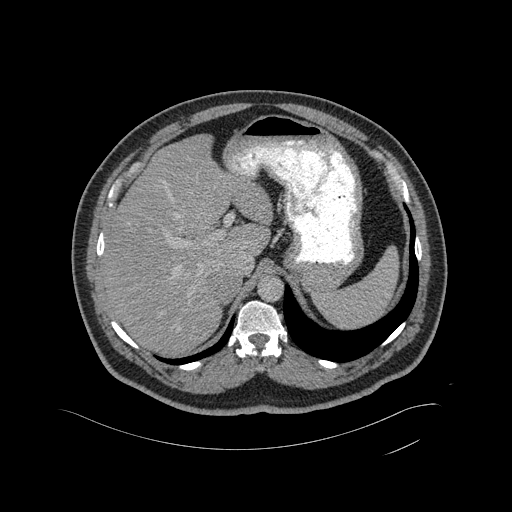
Contrast-enhanced abdominal CT, one axial slice; position 343 of 433 along the scan axis; intravenous contrast given; soft-tissue window (W 400 / L 40 HU); 512 × 512 image matrix. Male patient, age 56 years. Case-level facts recorded for this patient, not image findings: diagnosis: adrenocortical carcinoma; tumour side: right adrenal; tumour size at pathology: 11.6 cm; Ki-67 index: 50 %; stage (as recorded): 3.
Annotated regions visible in this slice (semi-automatically segmented with operator editing):
- mass: bounding box [x1, y1, x2, y2] px = [211, 269, 238, 300]